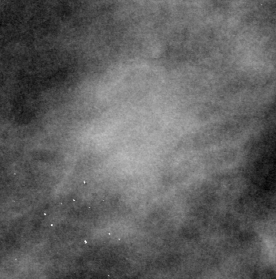
Region of interest cut from a scanned film mammogram (one marked finding), left breast, CC view.
- Finding: mass, shape round, margins ill defined; BI-RADS assessment category 3; subtlety rating 4 on a 1 (subtle) to 5 (obvious) scale; pathology (as recorded): benign.